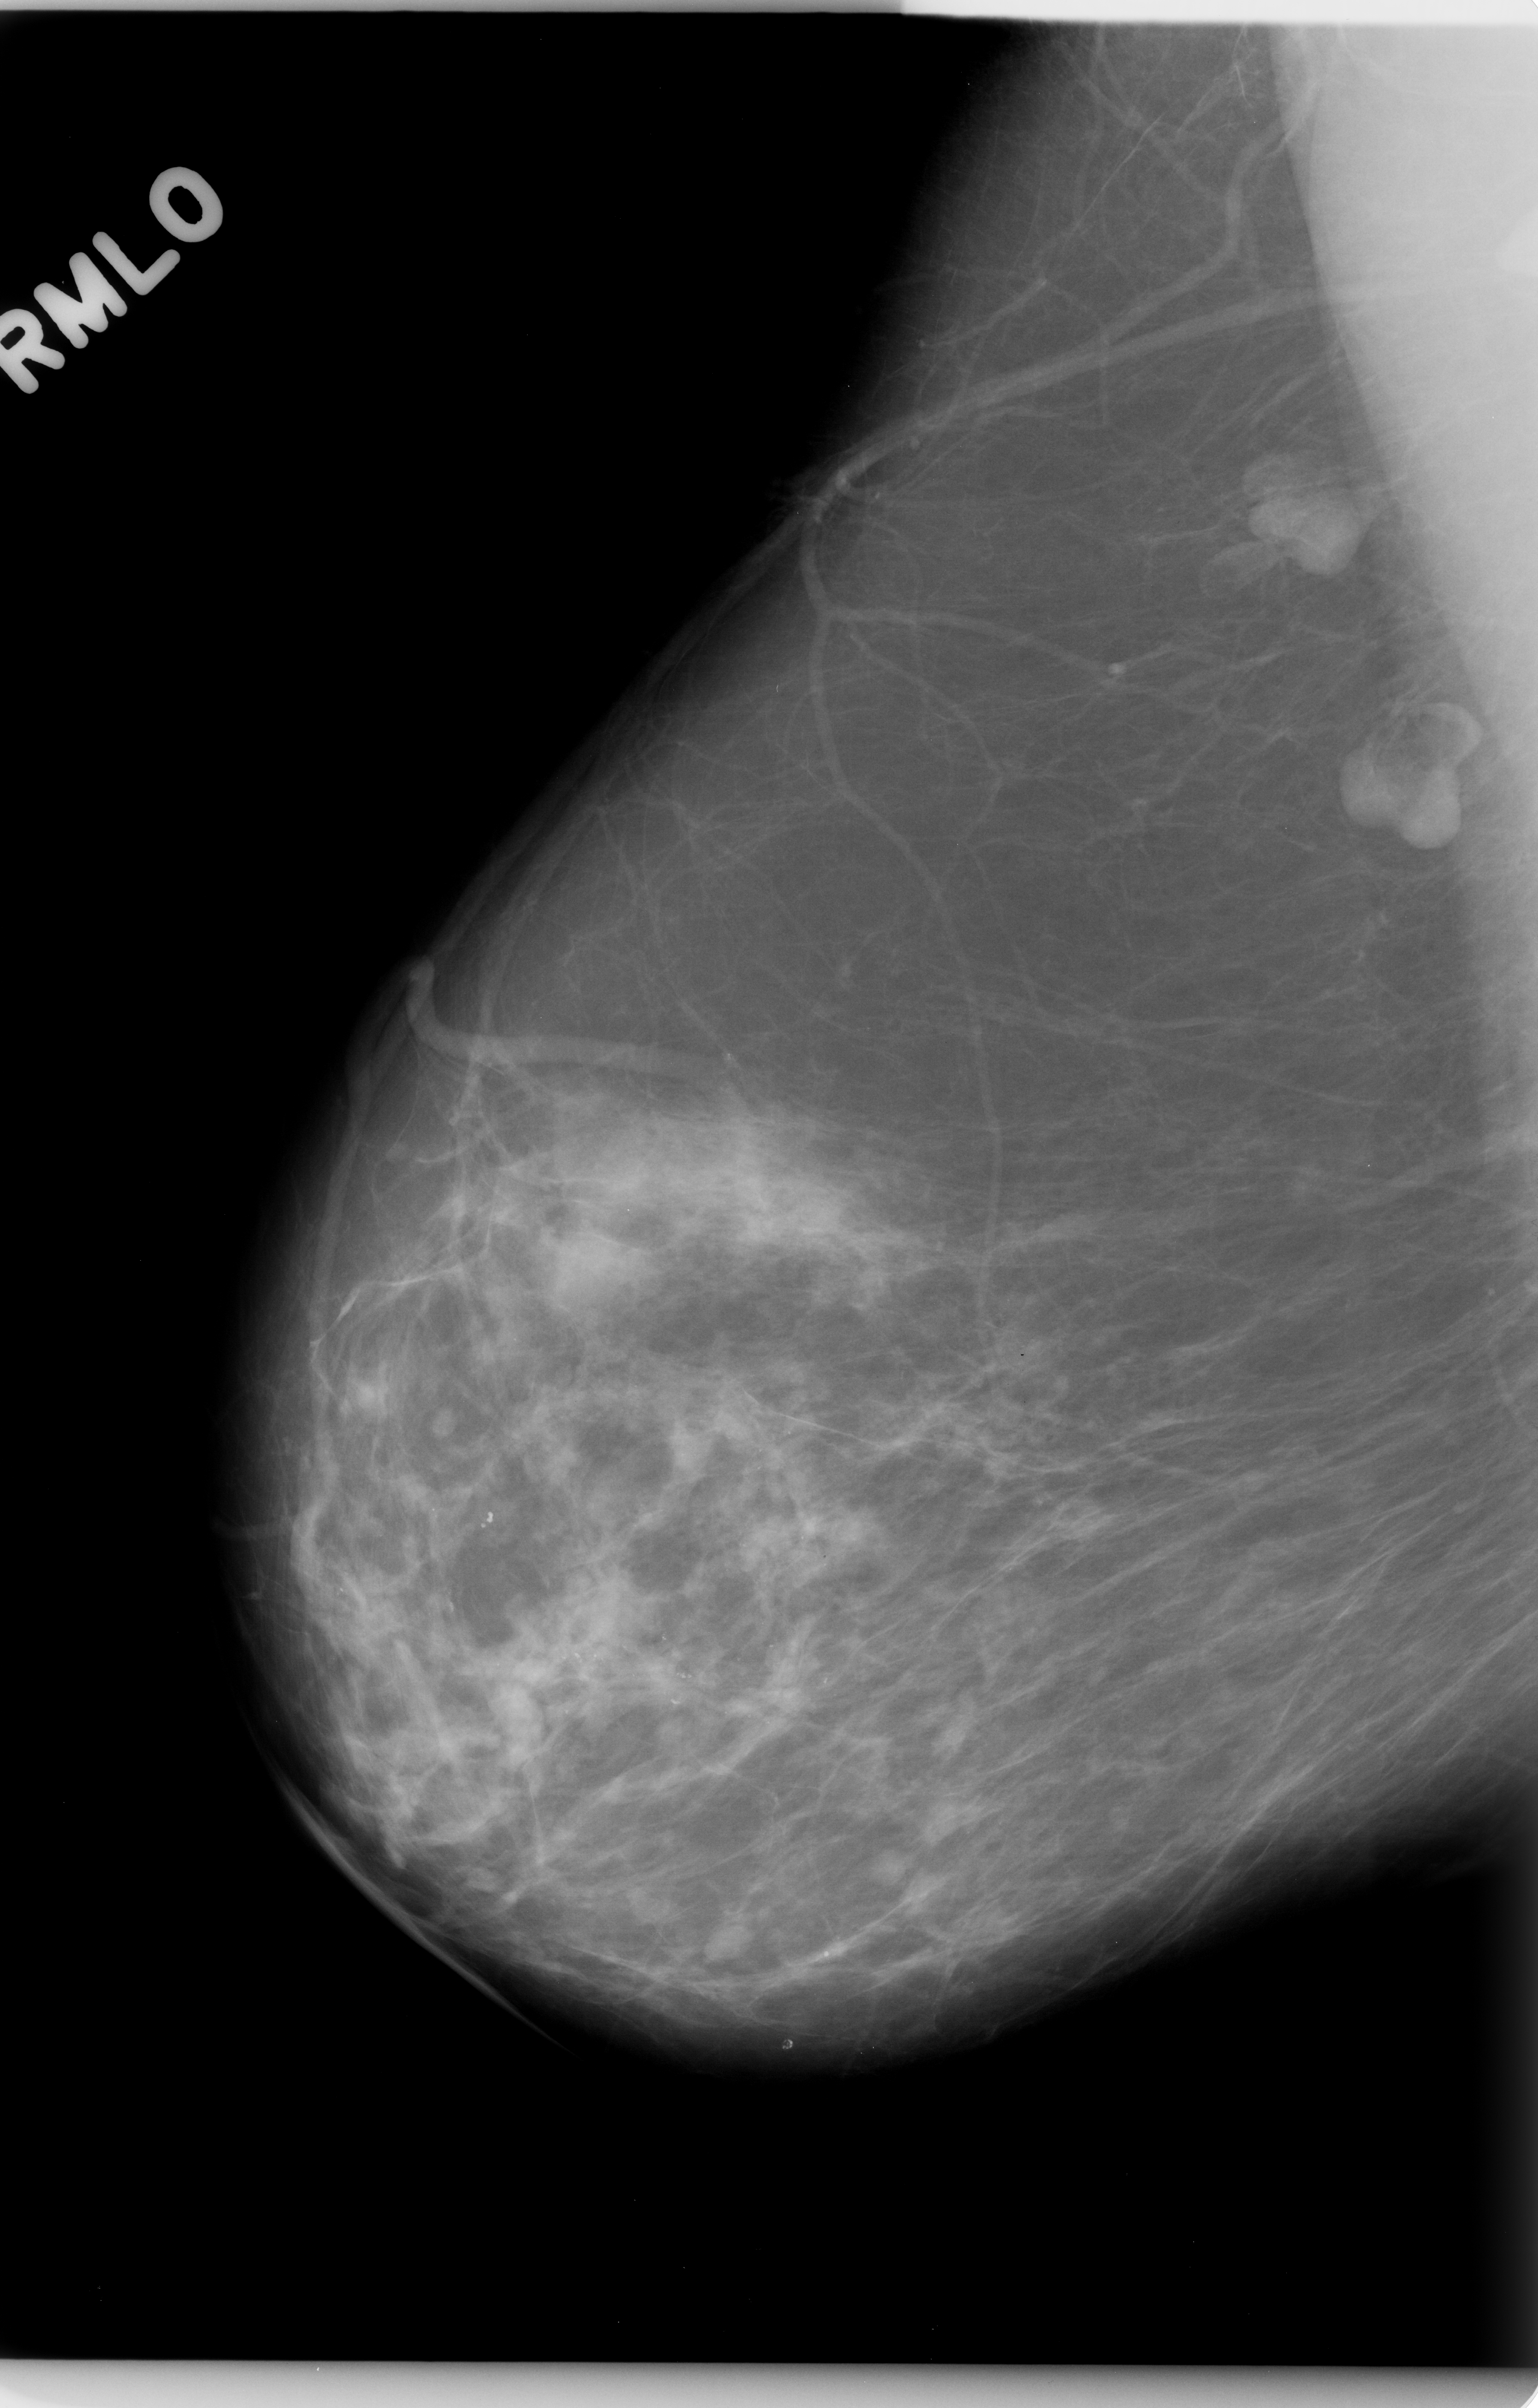
Scanned film-screen mammogram. Right breast. MLO view. BI-RADS breast density category 2 (scale 1–4). 1538 × 2408 image matrix.
Expert-marked regions of interest on this film, with their recorded descriptors:
- calcifications, morphology pleomorphic, distribution segmental; BI-RADS assessment category 4; subtlety rating 4 on a 1 (subtle) to 5 (obvious) scale; pathology (as recorded): malignant: bounding box <443,1378,995,1809> (left, top, right, bottom; pixels)